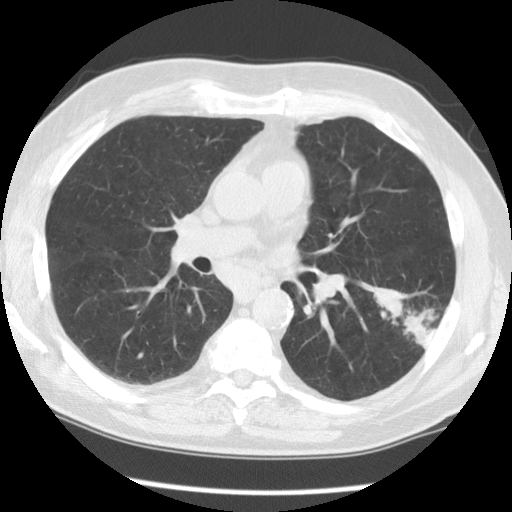
Low-dose screening chest CT, one axial slice; slice 75 of 130 in the series (ordered by position); reconstruction kernel STANDARD; lung window (W 1500 / L -600 HU); 2.5 mm slice thickness; 512 × 512 image matrix.
Outlined on this slice (manually delineated by an expert):
- lesion 1 (tumor, lower lobe of left lung): box from (x=375, y=290) to (x=437, y=348) px